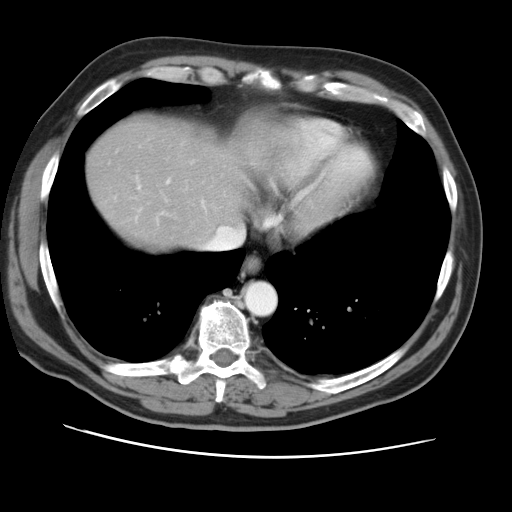
Contrast-enhanced abdominal CT, one axial slice; position 44 of 49 along the scan axis; 120 kVp; intravenous contrast given; soft-tissue window (W 400 / L 40 HU); 512 × 512 image matrix, field of view 374 × 374 mm. Male patient, age 59 years. Case-level facts recorded for this patient, not image findings: diagnosis: colorectal cancer liver metastases, imaged before liver resection; multiple liver metastases: yes; largest metastasis: 6.3 cm.
Structures marked on this image (expert manual segmentation):
- hepatic veins: bounding box (x1, y1, x2, y2) in pixels: (204, 226, 244, 249)
- liver: (88, 122, 248, 249)
- planned liver remnant (the part of the liver to remain after resection): (88, 122, 248, 249)
- portal vein (with intrahepatic branches): (167, 180, 204, 207)